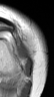
MRI of an extremity soft-tissue mass, one axial slice. Position 16 of 42 along the scan axis. MR volume resampled by the dataset authors to the PET/CT grid (not the native acquisition matrix). 3.27 mm slice thickness. 54 × 97 image matrix, field of view 53 × 95 mm. Female patient. Case-level facts recorded for this patient, not image findings: histological type: spindle cell suggestive of biphasic synovial sarcoma; grade: intermediate; site of the primary tumour: left knee.
Structures marked on this image (expert contour drawn on MRI and transferred to this co-registered scan by the dataset authors):
- gross tumour volume including surrounding oedema: bounding box <15,44,31,75> (left, top, right, bottom; pixels)
- gross tumour volume (mass): <15,46,31,75>